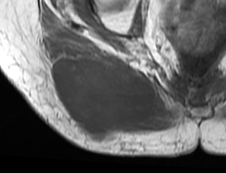
MRI of an extremity soft-tissue mass, one axial slice; position 32 of 73 along the scan axis; MR volume resampled by the dataset authors to the PET/CT grid (not the native acquisition matrix); 3.27 mm slice thickness; 226 × 173 image matrix, field of view 221 × 169 mm. Female patient. Case-level facts recorded for this patient, not image findings: histological type: spindle cell suggestive of myxofibrosarcoma; grade: intermediate; site of the primary tumour: right buttock.
Annotated regions visible in this slice (expert contour drawn on MRI and transferred to this co-registered scan by the dataset authors):
- gross tumour volume (mass): bounding box [x1, y1, x2, y2] px = [49, 42, 156, 141]